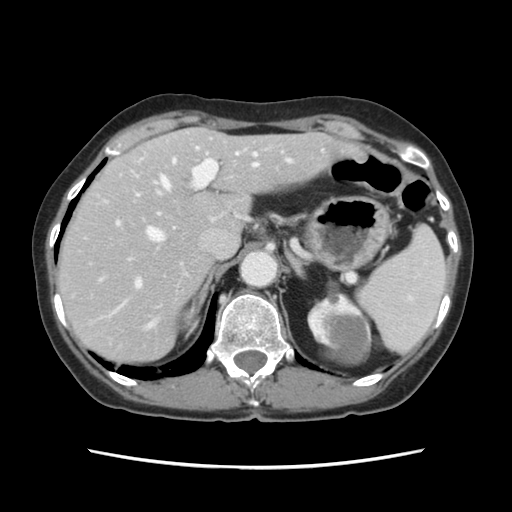
Contrast-enhanced abdominal CT, one axial slice. Position 86 of 120 along the scan axis. 120 kVp. Intravenous contrast given. Soft-tissue window (W 400 / L 40 HU). 512 × 512 image matrix, field of view 330 × 330 mm. Female patient, age 70 years. Case-level facts recorded for this patient, not image findings: diagnosis: colorectal cancer liver metastases, imaged before liver resection; multiple liver metastases: no; largest metastasis: 2.5 cm.
Structures marked on this image (manually delineated by an expert):
- hepatic veins: bounding box [x1, y1, x2, y2] px = [147, 153, 258, 325]
- liver: [59, 128, 347, 362]
- planned liver remnant (the part of the liver to remain after resection): [109, 128, 346, 291]
- portal vein (with intrahepatic branches): [100, 147, 291, 288]